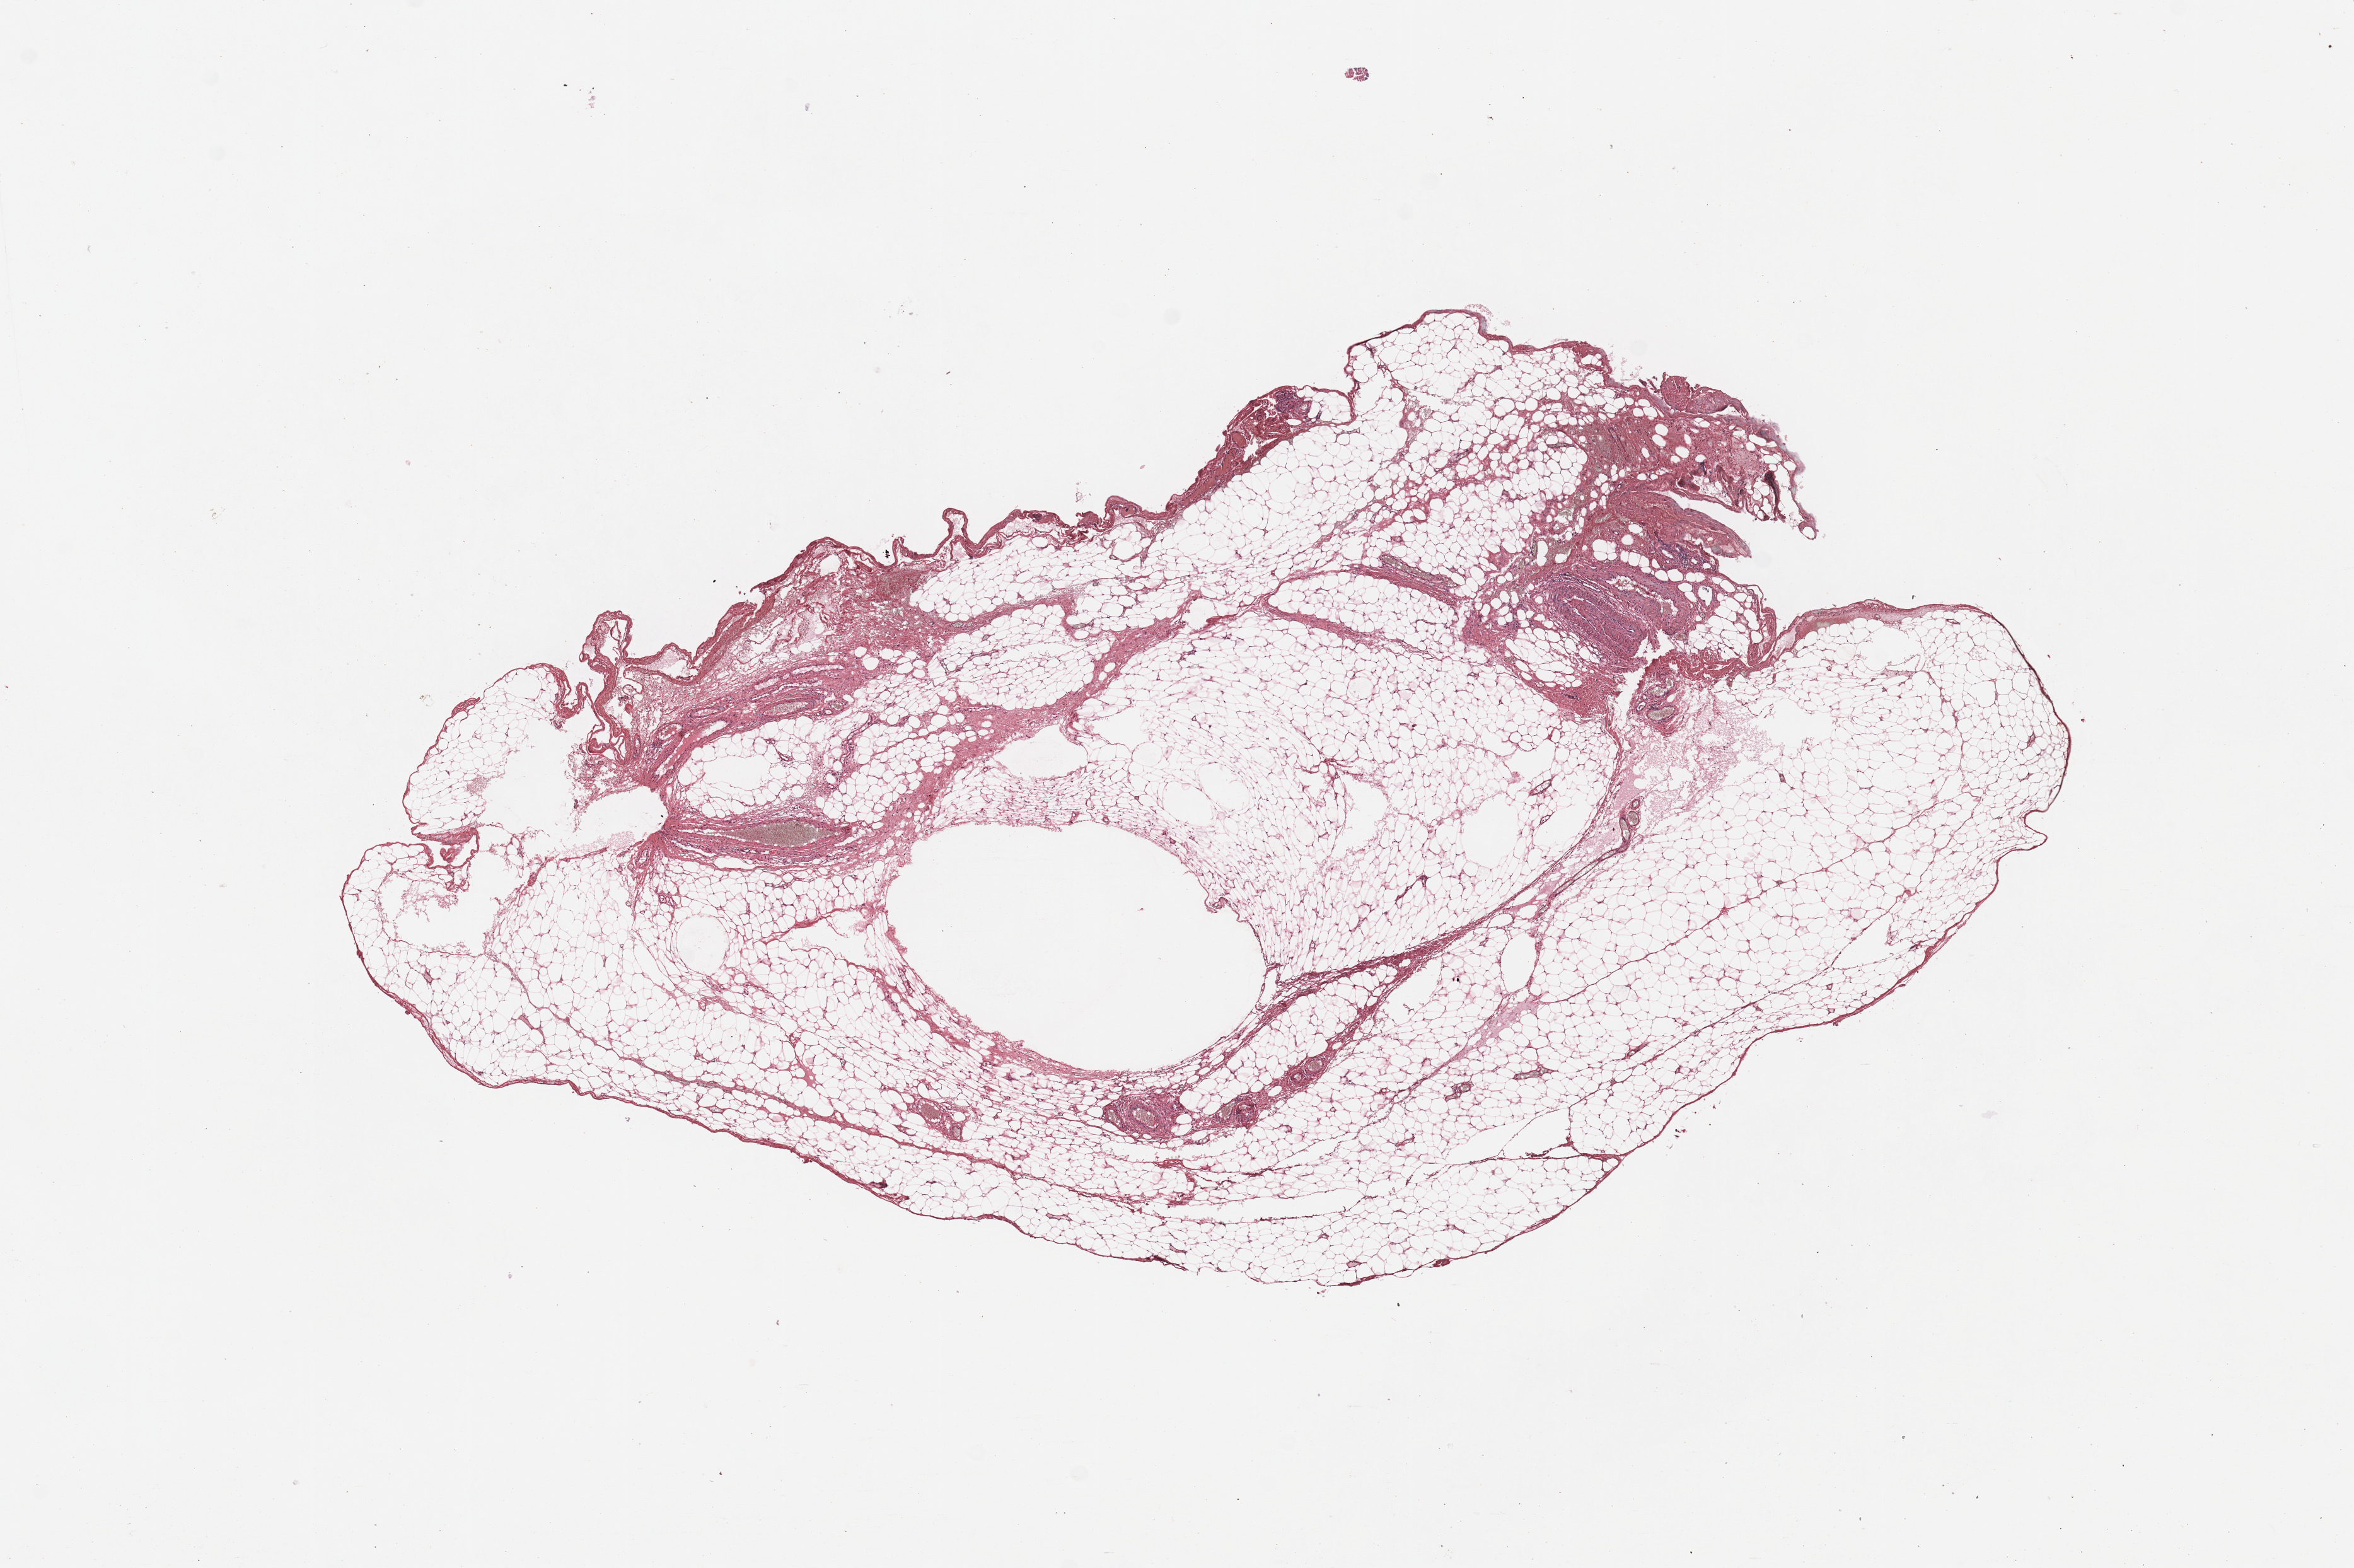
Digitized Hematoxylin and eosin (H&E) stained tissue section (whole slide) — a low-resolution overview of the entire scanned area, about 14.8 x 9.8 mm (slide scanned at 20x), normal (non-tumour) tissue sample. 65-year-old female patient.
This section: normal (non-tumour) tissue from the same patient. Patient diagnosis (cohort enrolment): sarcoma (site not recorded at cohort level).